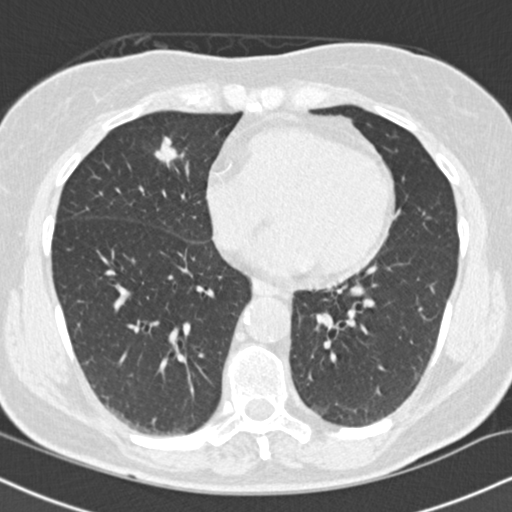
Chest CT (low-dose screening protocol), one axial image; first (baseline) screen; lung window (W 1500 / L -600 HU); 2 mm slice thickness; 512 × 512 image matrix, field of view 320 × 320 mm. Female, age 66 years at enrolment. Current smoker at enrolment.
- Lesion marked by an expert reader, bounding box <140,130,184,170> (left, top, right, bottom; pixels).
- Reader record for this screening exam (exam-level; its link to the box is not recorded): non-calcified nodule or mass ≥4 mm, right lower lobe, 10 × 8 mm, smooth margins, soft tissue attenuation.
- Lung cancer was diagnosed 96 days after this screen: squamous cell carcinoma, keratinizing, NOS, right upper lobe, right middle lobe, poorly differentiated (G3), stage IA (AJCC 6th edition), 14 mm at pathology.